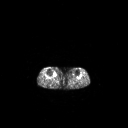
FDG PET of an extremity soft-tissue mass (from a PET/CT study), one axial slice; position 153 of 267 along the scan axis; 3.27 mm slice thickness; 128 × 128 image matrix, field of view 700 × 700 mm. Female patient, age 65 years. From the clinical record (not read from this slice): histological type: undifferentiated – high grade; grade: high; site of the primary tumour: right thigh.
Structures marked on this image (expert contour drawn on MRI and transferred to this co-registered scan by the dataset authors):
- gross tumour volume (mass): bounding box <53,72,57,77> (left, top, right, bottom; pixels)